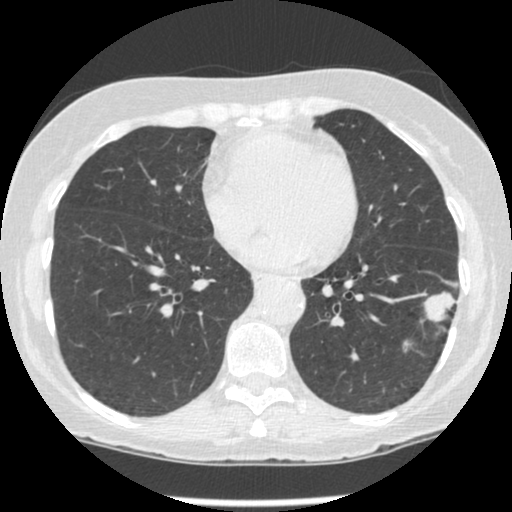
Low-dose screening chest CT, one axial slice; position 98 of 247 along the scan axis; 120 kVp; lung window (W 1500 / L -600 HU); 1.25 mm slice thickness; 512 × 512 image matrix, field of view 303 × 303 mm.
Annotated regions visible in this slice (manually delineated by an expert):
- lesion 1 (tumor, lower lobe of left lung): bounding box [x1, y1, x2, y2] px = [423, 292, 456, 323]